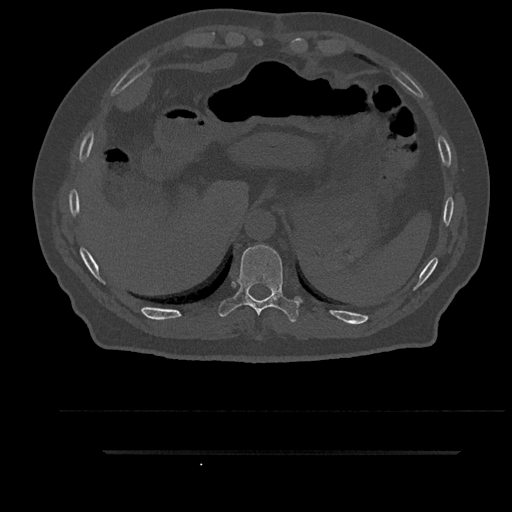
CT including the spine, one axial slice. Position 370 of 797 along the scan axis. Reconstruction kernel Br40s/3. 120 kVp. Bone window (W 1800 / L 400 HU). 512 × 512 image matrix. Patient: male, 63 years. From the clinical record (not read from this slice): primary cancer: renal; vertebrae with lytic lesions (as recorded): T8.
Outlined on this slice (semi-automatically segmented with operator editing):
- T10 vertebra: bounding box <218,245,302,322> (left, top, right, bottom; pixels)